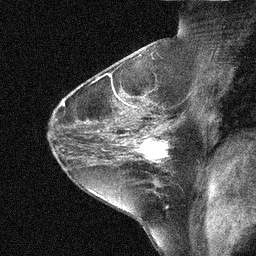
Breast MRI (dynamic contrast-enhanced), one sagittal slice; position 27 of 44 along the scan axis; dynamic contrast-enhanced study with each time point stored as its own series, time point 2 of 3 at this slice position (early post-contrast, ordered by acquisition time); 1.5 T; TE 5 ms, TR 10.3 ms; 3 mm slice thickness; 256 × 256 image matrix, field of view 180 × 180 mm. Patient: female, 31 years. Case-level facts recorded for this patient, not image findings: setting: breast cancer imaged before/during neoadjuvant chemotherapy; receptor status: HER2-positive.
Annotated regions visible in this slice (semi-automatic segmentation, software-assisted and operator-edited):
- analysis volume of interest (the breast-tissue region the enhancement analysis was run in; not a lesion): bounding box (x1, y1, x2, y2) in pixels: (136, 131, 181, 168)
- tumour enhancement mask (voxels above the 90 % enhancement threshold inside the analysis volume of interest): (136, 138, 169, 162)